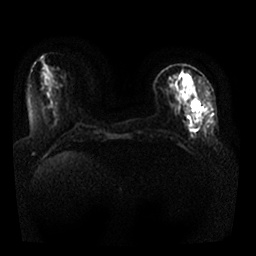
Breast MRI, one axial slice. Position 8 of 25 along the scan axis. Diffusion-weighted series; image 2 of 4 stored at this slice position (different b-values; order by instance number). 1.5 T. 256 × 256 image matrix. Female patient.
Outlined on this slice (manually delineated by an expert):
- tumour on diffusion-weighted imaging: bounding box (x1, y1, x2, y2) in pixels: (193, 101, 199, 110)